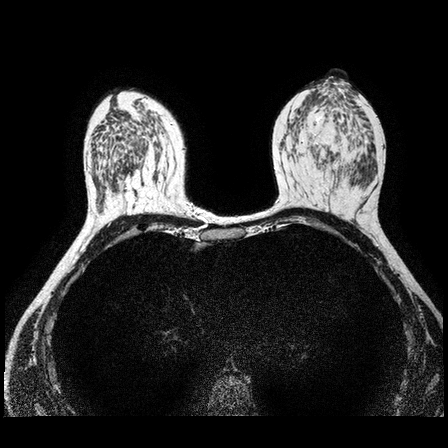
Breast MRI examination; 2 images, each one mid-volume slice chosen by position.
Image 1: axial T2-weighted / STIR image, slice 43 of 84.
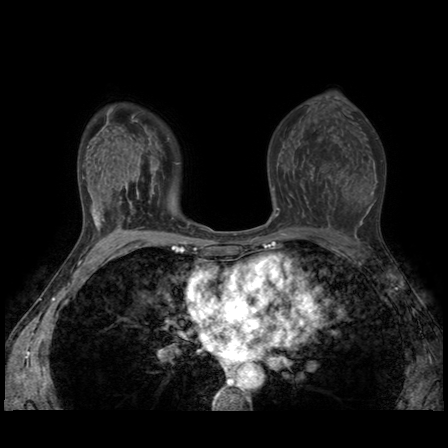
Image 2: post-contrast dynamic axial slice, slice 43 of 84, dynamic phase 5 of 8.
Patient-level pathology facts (from the clinical record, not from the images): pathology diagnosis: benign fibrocyst (left breast).